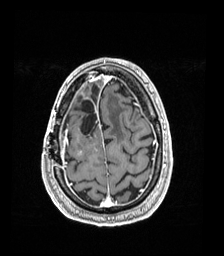
Brain MRI from a brain-tumour surgery series, one axial slice. Slice 40 of 192 in the series (ordered by position). T1-weighted post-contrast. 1 mm slice thickness. 224 × 256 image matrix, field of view 224 × 256 mm. From the clinical record (not read from this slice): histopathology: Astrocytoma; WHO grade: 4; IDH mutation: yes; tumour location: Right Frontal.
Structures marked on this image (expert manual segmentation):
- previous resection cavity: bounding box <74,100,97,136> (left, top, right, bottom; pixels)
- tumour: <78,91,84,155>